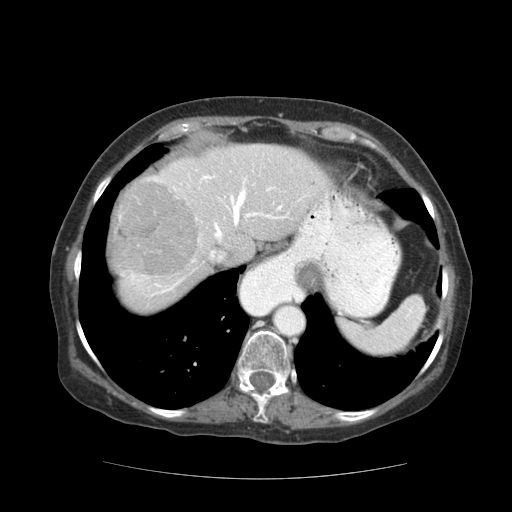
Contrast-enhanced abdominal CT (liver protocol), one axial slice. Position 92 of 111 along the scan axis. 140 kVp. Soft-tissue window (W 400 / L 40 HU). 512 × 512 image matrix. From the clinical record (not read from this slice): diagnosis: hepatocellular carcinoma (patient treated with transarterial chemoembolisation; whether this scan precedes or follows treatment is not stated here); TNM stage (as recorded): Stage-I; Child-Pugh class: A; tumour nodularity: uninodular.
Structures marked on this image (semi-automatic segmentation, software-assisted and operator-edited):
- abdominal aorta: bounding box [x1, y1, x2, y2] px = [275, 305, 304, 334]
- liver parenchyma outside the tumour (the mass and vessels are separate outlines, so this box may not span the whole liver): [110, 144, 330, 312]
- mass: [115, 179, 197, 278]
- liver vessels: [131, 175, 301, 296]